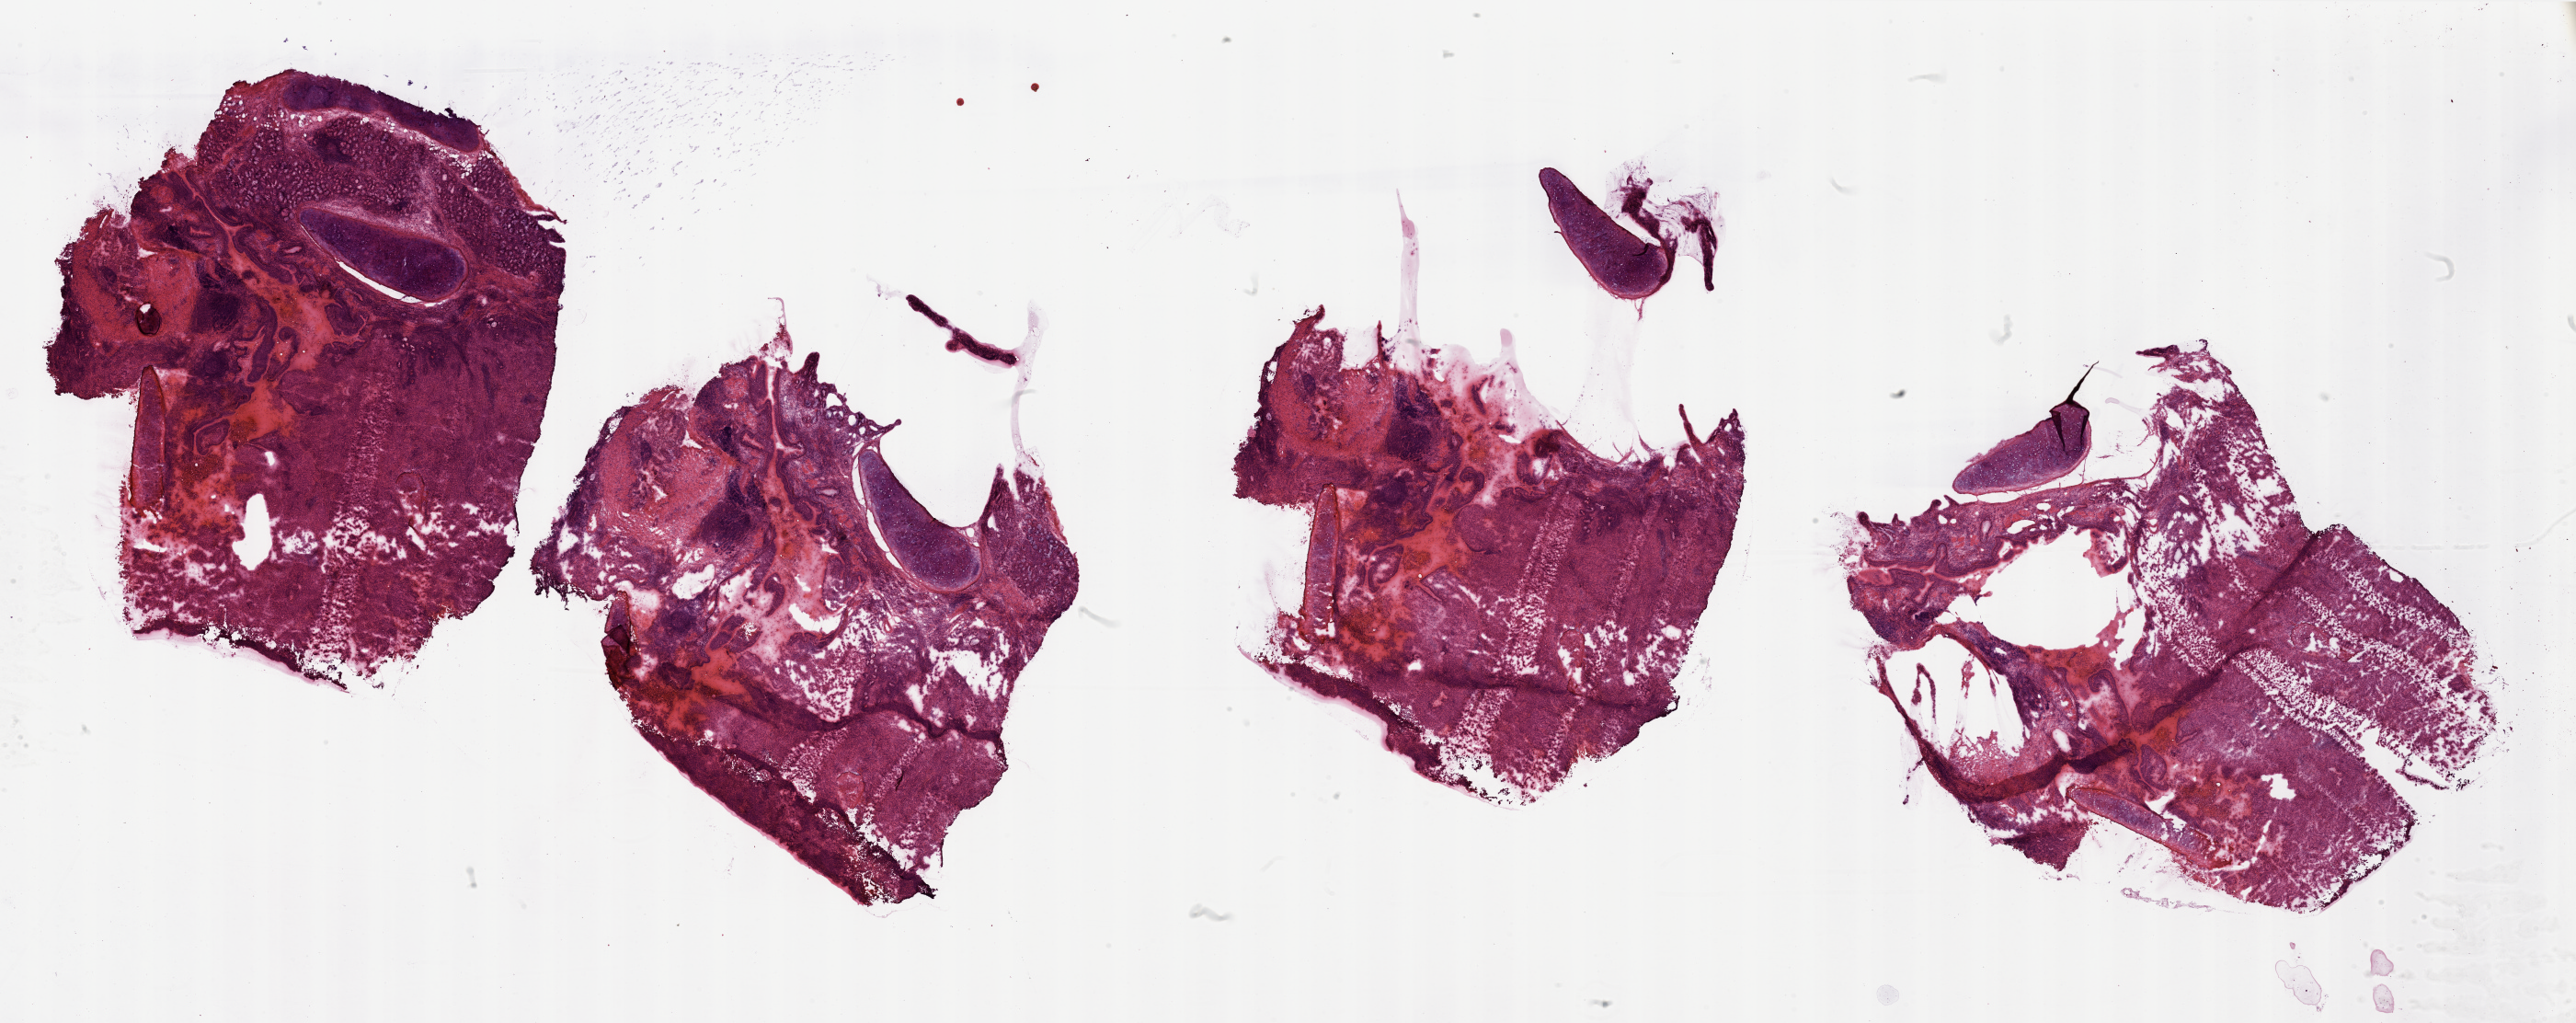
H&E whole-slide image, low-resolution overview of the scanned area, about 44.3 x 17.6 mm (acquisition: 20x scan), tumour tissue sample, lung. Male, 57 y/o. Histologic grade: GX (grade cannot be assessed).
Diagnosis: Adenocarcinoma, NOS. Primary tumour site (as recorded): right lower lobe. AJCC pathologic stage: IIB.